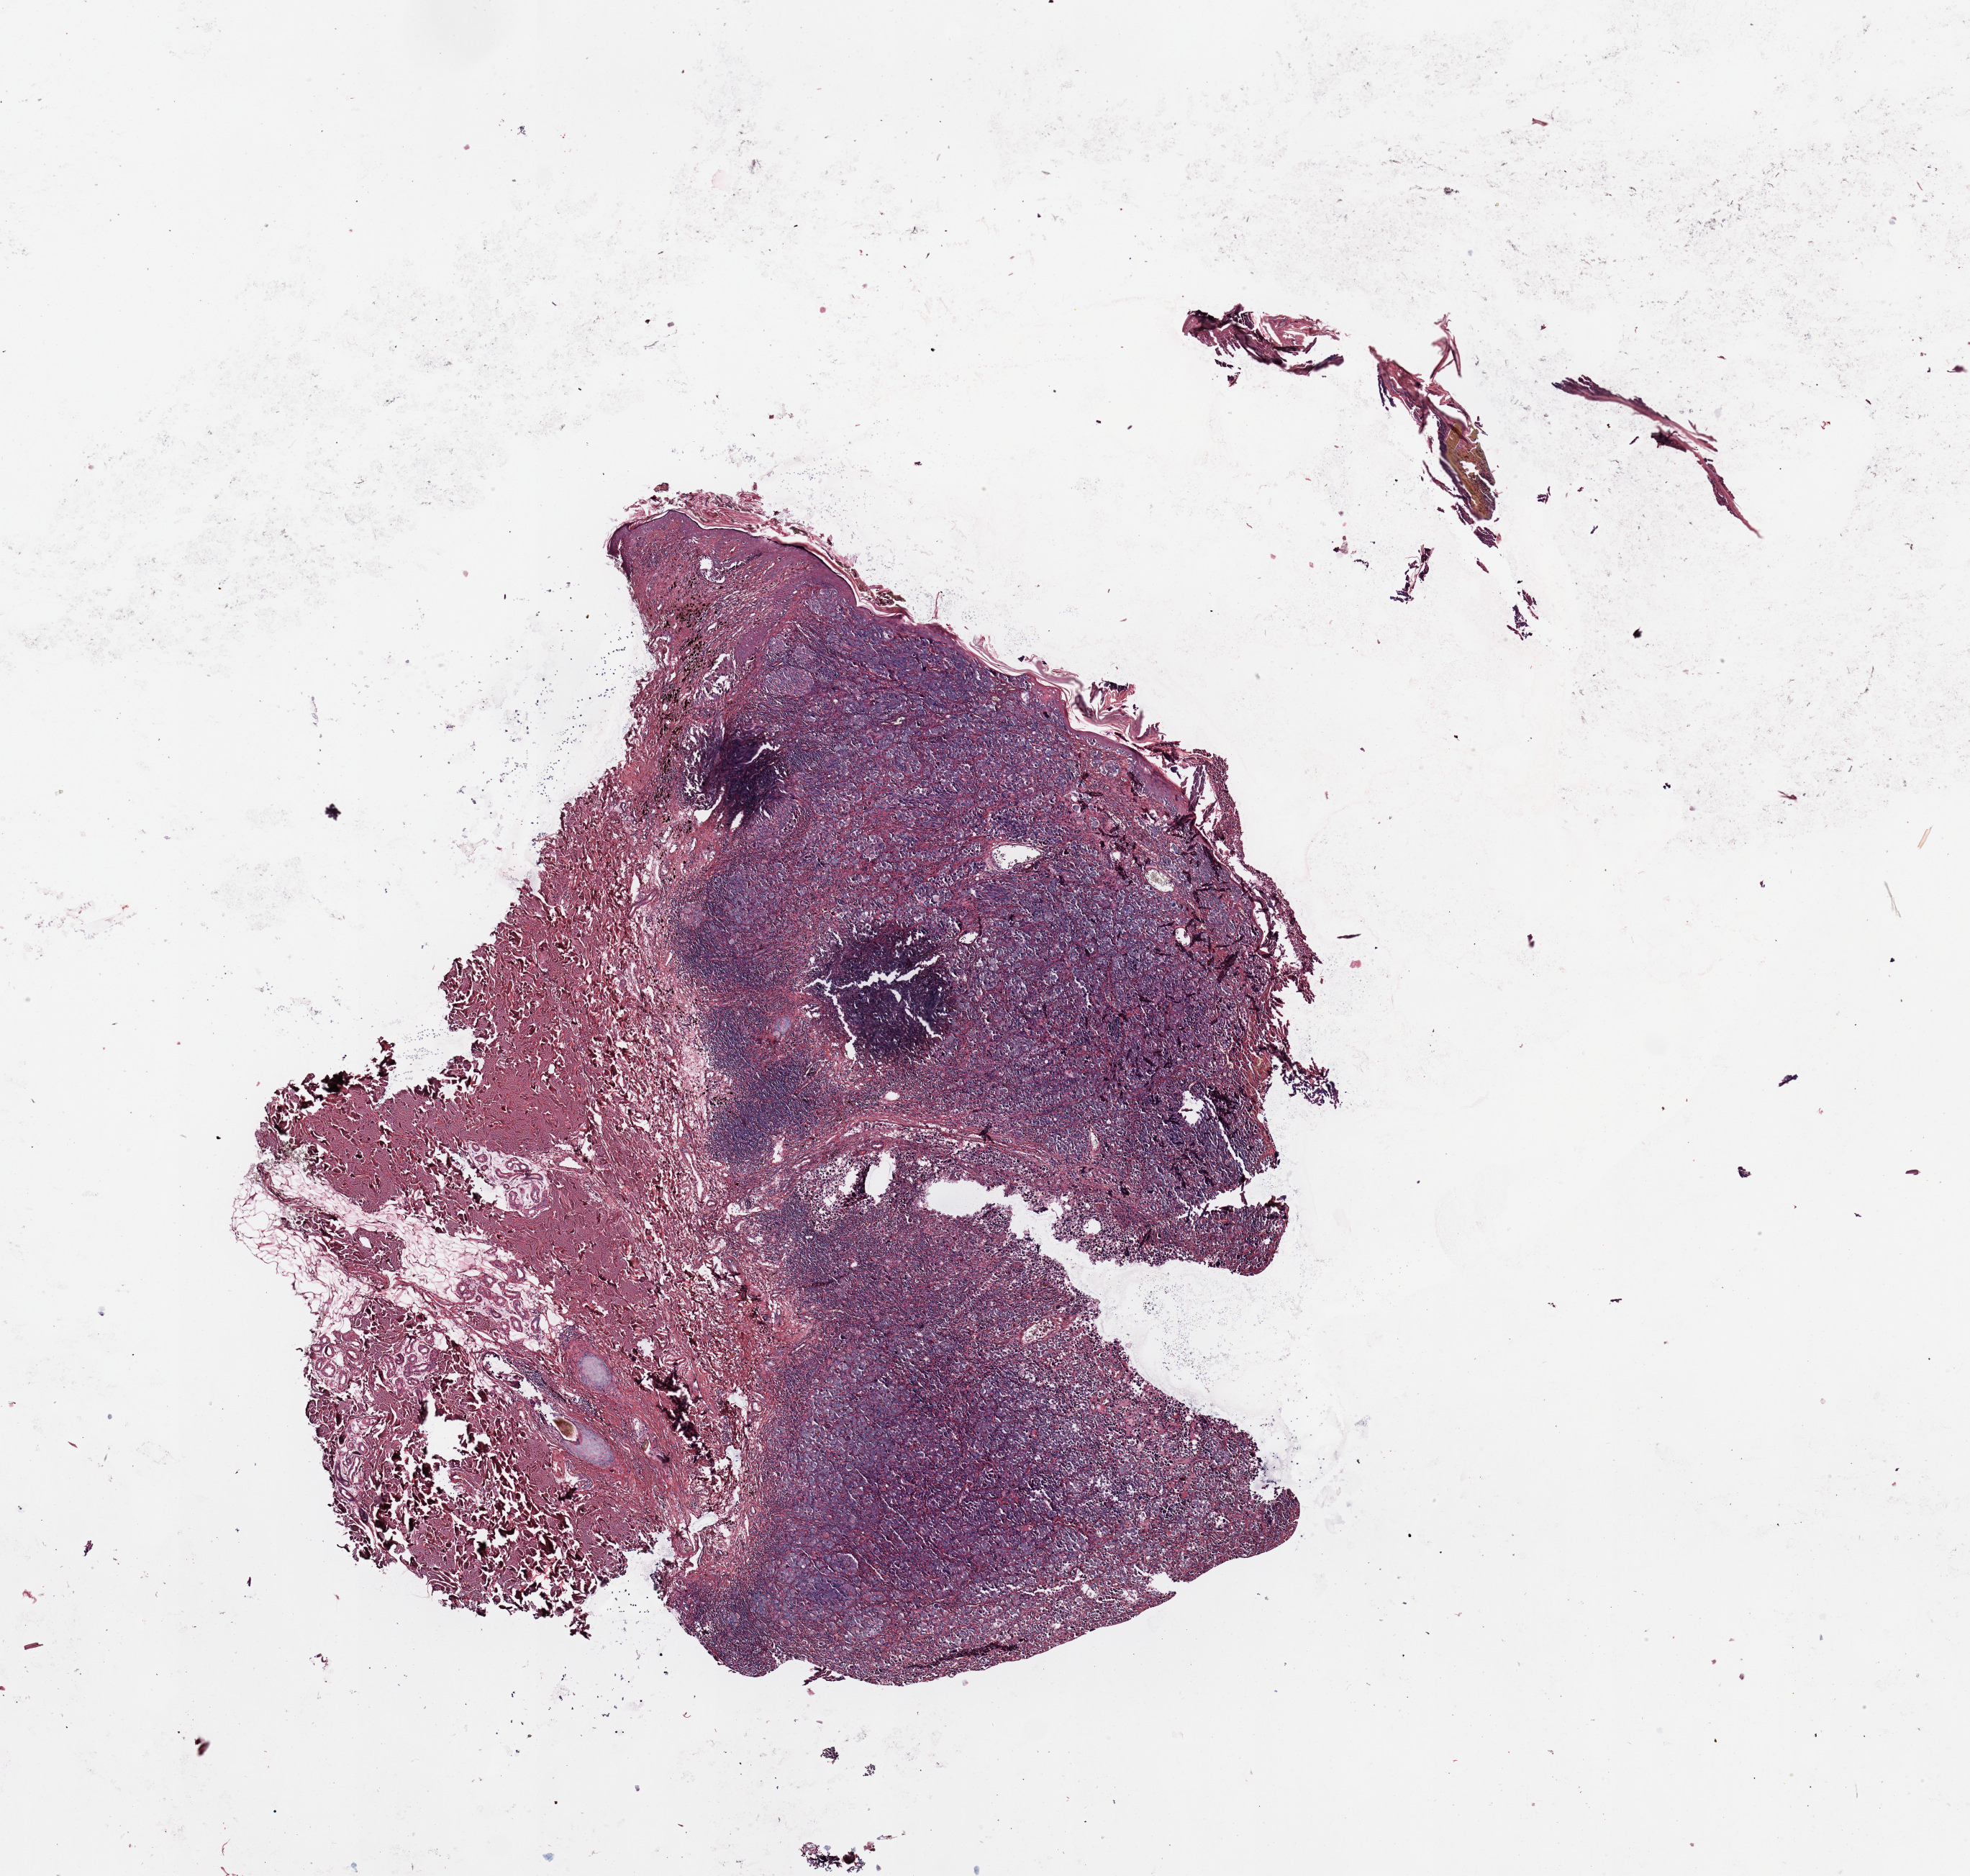
Whole-slide histology image, H&E — a low-resolution overview of the entire scanned area, about 10.8 x 10.3 mm (slide scanned at 20x), melanoma tumour tissue; sampled site not recorded. 83-year-old male patient.
AJCC pathologic stage: IIB. Histologic diagnosis: Malignant melanoma, NOS. Primary tumour site (as recorded): trunk.